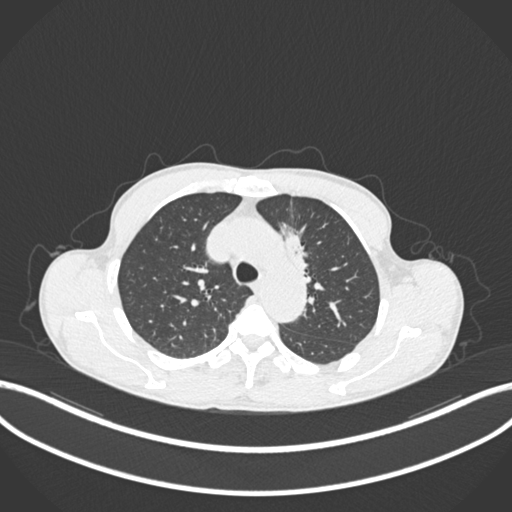
Chest CT, one axial slice; position 145 of 211 along the scan axis; lung window (W 1500 / L -600 HU); 512 × 512 image matrix, field of view 400 × 400 mm. Patient: male, 58 years. From the clinical record (not read from this slice): clinical TNM (as recorded): T1c N1 M0.
Outlined on this slice (bounding box drawn by a radiologist):
- lung tumour (recorded histology: adenocarcinoma): bounding box <275,223,313,288> (left, top, right, bottom; pixels)